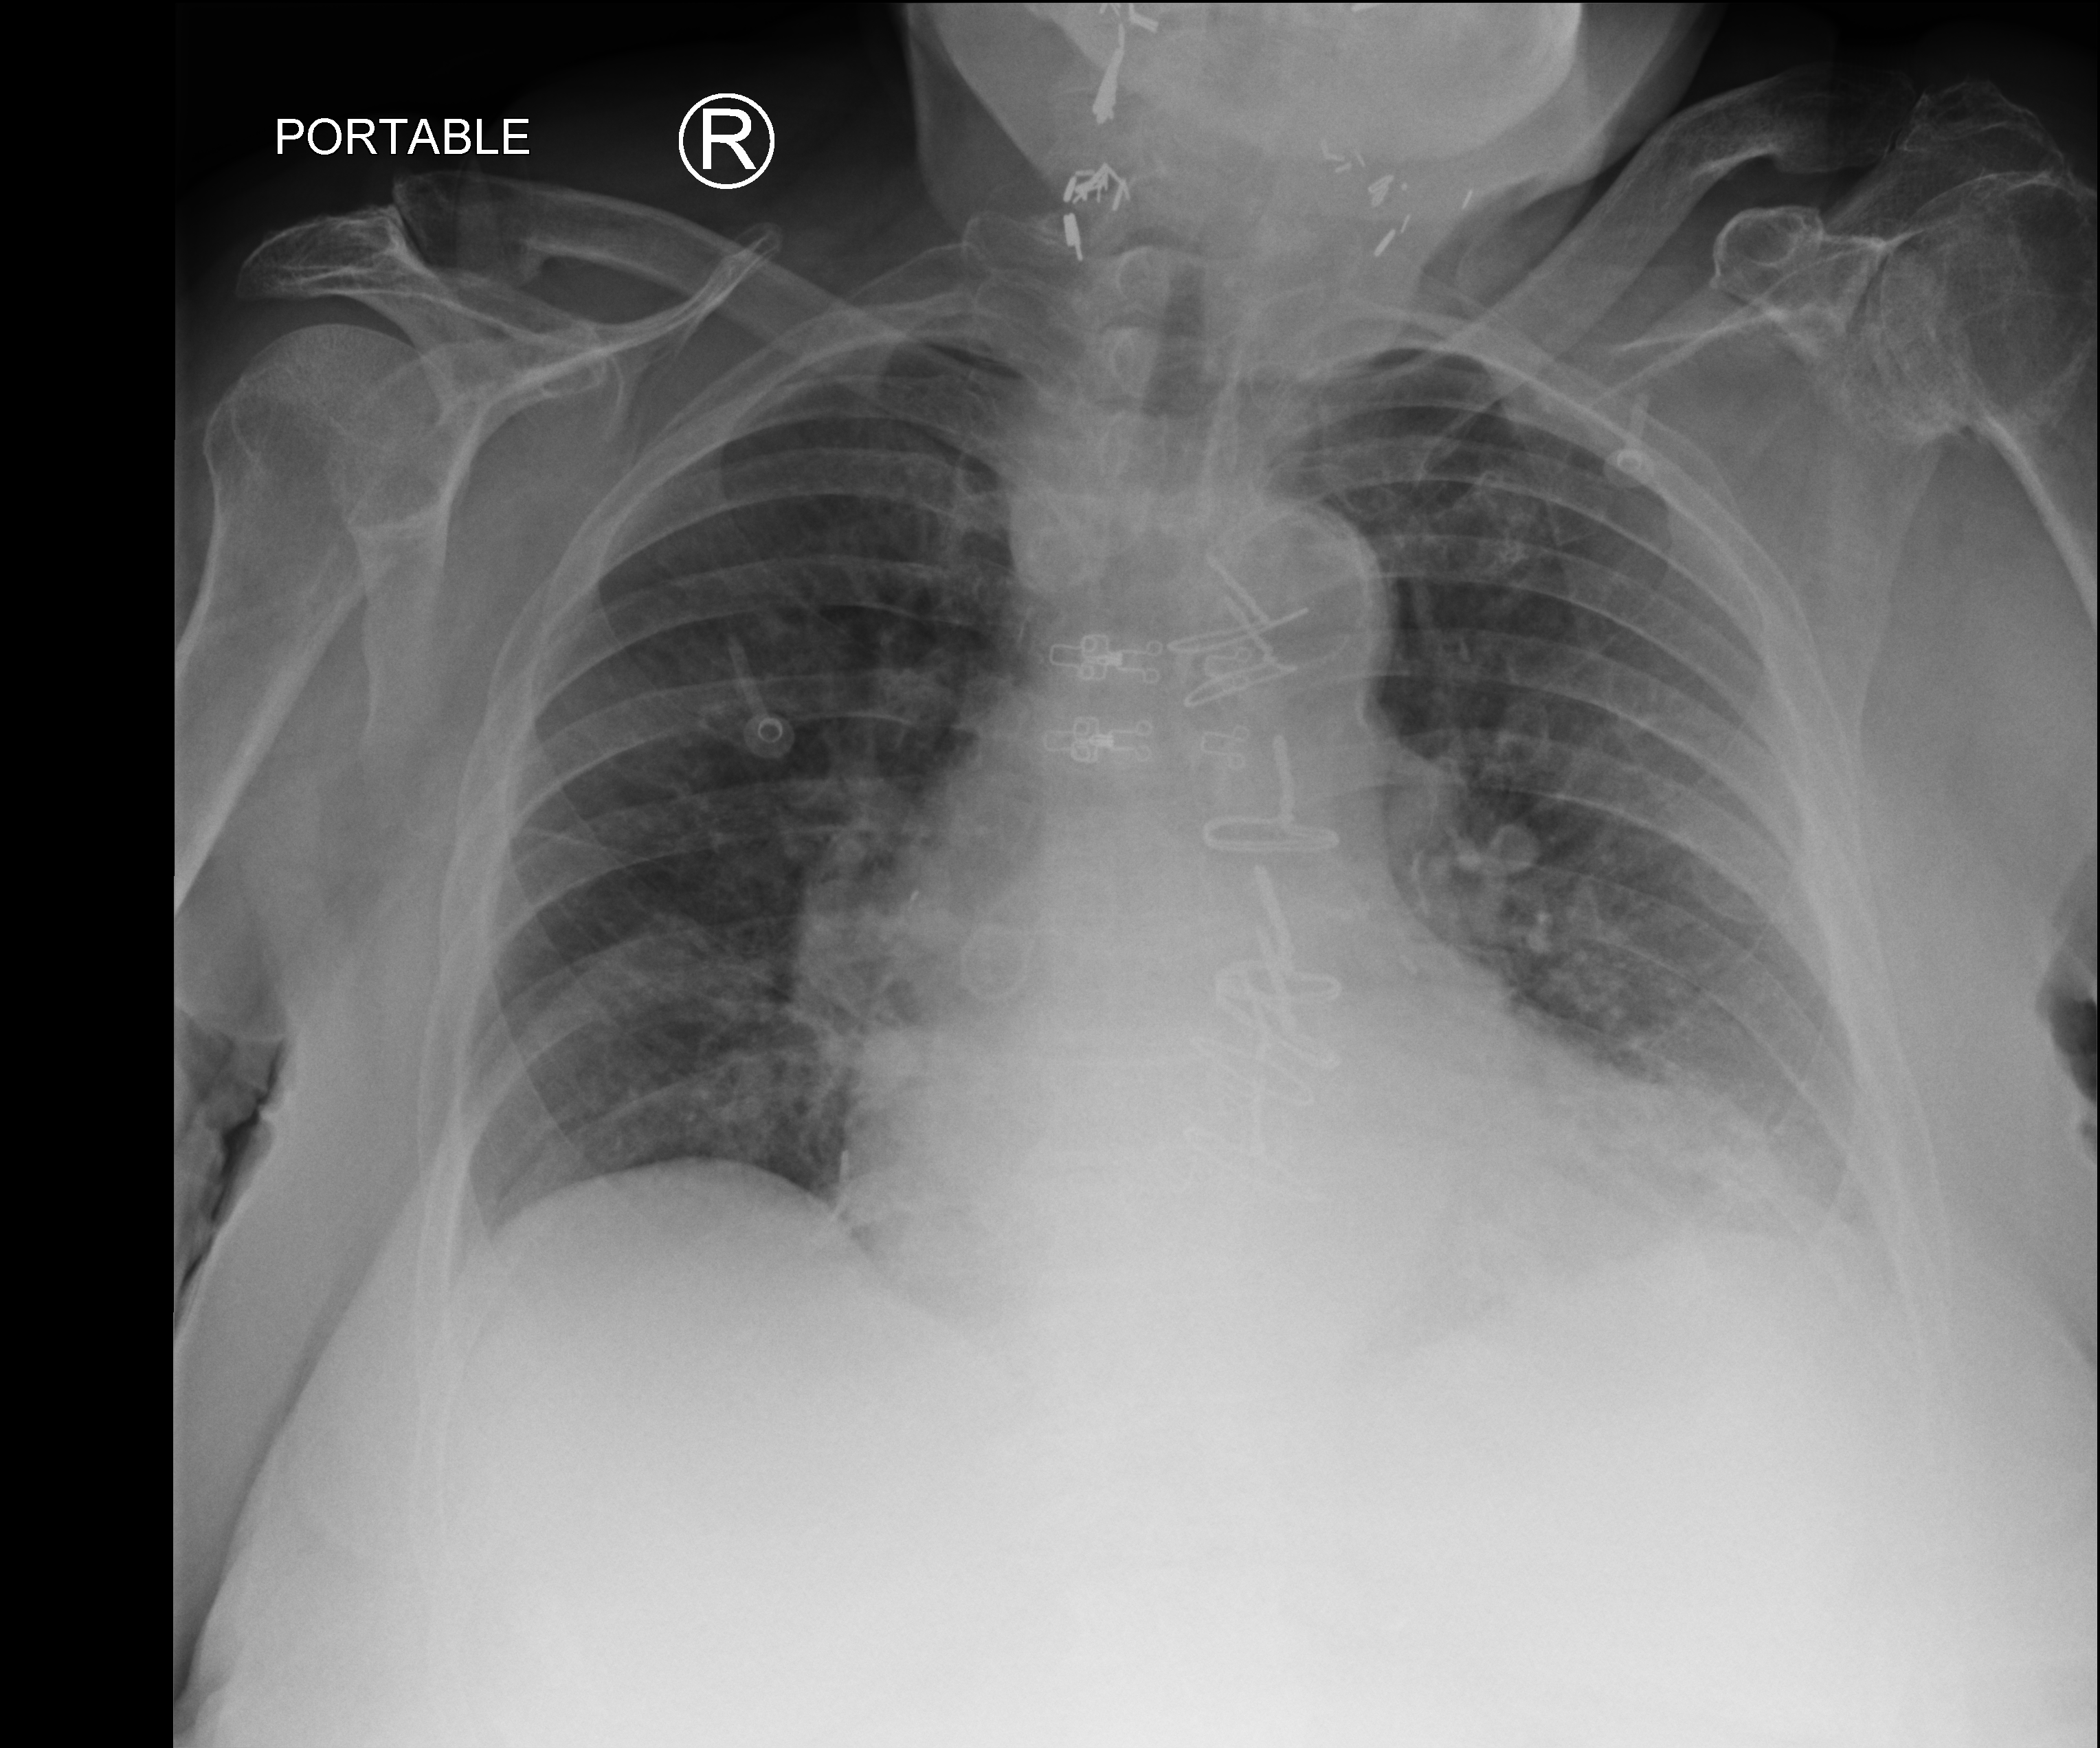
Chest X-ray (portable), anteroposterior (AP) projection. Patient hospitalised with COVID-19; female, aged 75–90 years.
From the hospital-stay record, not from the radiograph (when in the stay this image was taken is not recorded):
- admitted to intensive care during this hospital stay: no
- other chronic lung disease (admission record): yes